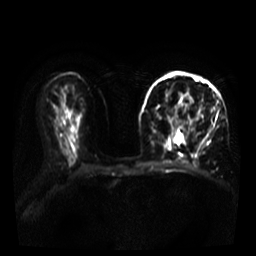
Breast MRI, one axial slice; position 18 of 39 along the scan axis; diffusion-weighted series; image 2 of 4 stored at this slice position (different b-values; order by instance number); 3 T; 256 × 256 image matrix. Female patient.
Structures marked on this image (manually delineated by an expert):
- tumour on diffusion-weighted imaging: bounding box [x1, y1, x2, y2] px = [179, 94, 193, 104]